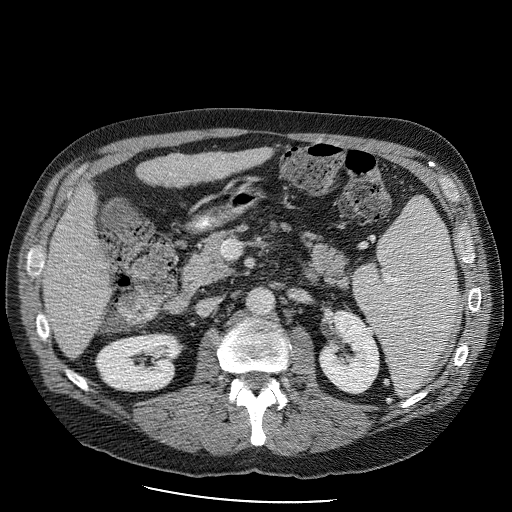
Contrast-enhanced abdominal CT (liver protocol), one axial slice; position 35 of 98 along the scan axis; reconstruction kernel STANDARD; 120 kVp; soft-tissue window (W 400 / L 40 HU); 2.5 mm slice thickness; 512 × 512 image matrix, field of view 400 × 400 mm. Case-level facts recorded for this patient, not image findings: diagnosis: hepatocellular carcinoma (patient treated with transarterial chemoembolisation; whether this scan precedes or follows treatment is not stated here); TNM stage (as recorded): Stage-II; Child-Pugh class: B; tumour differentiation: moderately differentiated.
Outlined on this slice (semi-automatically segmented with operator editing):
- liver parenchyma outside the tumour (the mass and vessels are separate outlines, so this box may not span the whole liver): box from (x=42, y=140) to (x=282, y=342) px
- liver vessels: (x=84, y=298)–(x=87, y=302)